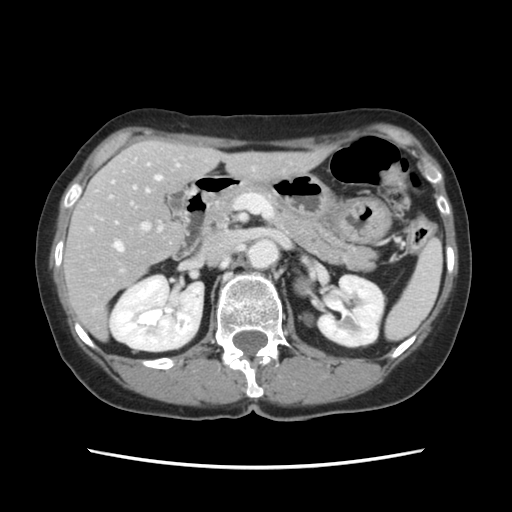
Contrast-enhanced abdominal CT, one axial slice. Intravenous contrast given. Soft-tissue window (W 400 / L 40 HU). 2.5 mm slice thickness. 512 × 512 image matrix, field of view 330 × 330 mm. Female patient, age 70 years. From the clinical record (not read from this slice): diagnosis: colorectal cancer liver metastases, imaged before liver resection; multiple liver metastases: no; largest metastasis: 2.5 cm; disease in both lobes: no.
Annotated regions visible in this slice (manually delineated by an expert):
- hepatic veins: bounding box <114,165,162,251> (left, top, right, bottom; pixels)
- liver: <65,141,323,337>
- planned liver remnant (the part of the liver to remain after resection): <78,141,324,279>
- portal vein (with intrahepatic branches): <110,164,254,231>